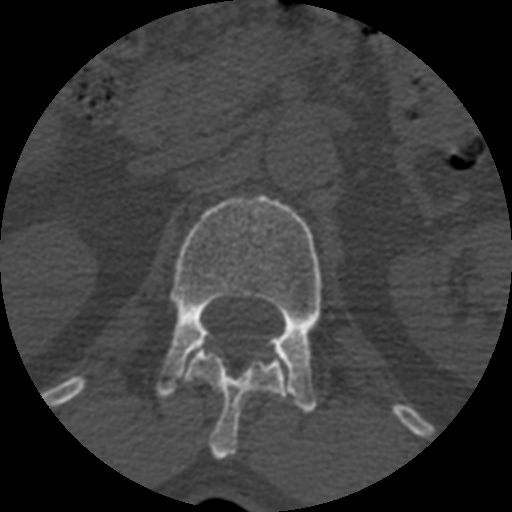
CT including the spine, one axial slice. Slice 369 of 399 in the series (ordered by position). Reconstruction kernel STANDARD. 120 kVp. Bone window (W 1800 / L 400 HU). 1.25 mm slice thickness. 512 × 512 image matrix. Patient age 71 years. From the clinical record (not read from this slice): primary cancer: prostate.
Annotated regions visible in this slice (semi-automatic segmentation, software-assisted and operator-edited):
- L1 vertebra: bounding box [x1, y1, x2, y2] px = [156, 195, 322, 412]
- T12 vertebra: [185, 348, 290, 461]